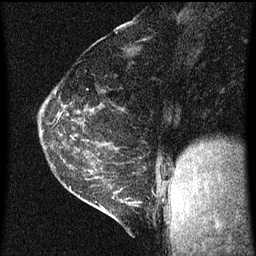
Breast MRI (dynamic contrast-enhanced), one sagittal slice. Position 22 of 60 along the scan axis. Dynamic contrast-enhanced series, image 2 of 3 at this slice position (ordered by acquisition). 1.5 T. TE 4.2 ms, TR 8 ms. 2 mm slice thickness. 256 × 256 image matrix, field of view 180 × 180 mm. Female patient, age 35 years.
Outlined on this slice (semi-automatic segmentation, software-assisted and operator-edited):
- analysis volume of interest (the breast-tissue region the enhancement analysis was run in; not a lesion): bounding box <106,182,143,223> (left, top, right, bottom; pixels)
- tumour enhancement mask (voxels above the 70 % enhancement threshold inside the analysis volume of interest): <106,190,137,211>